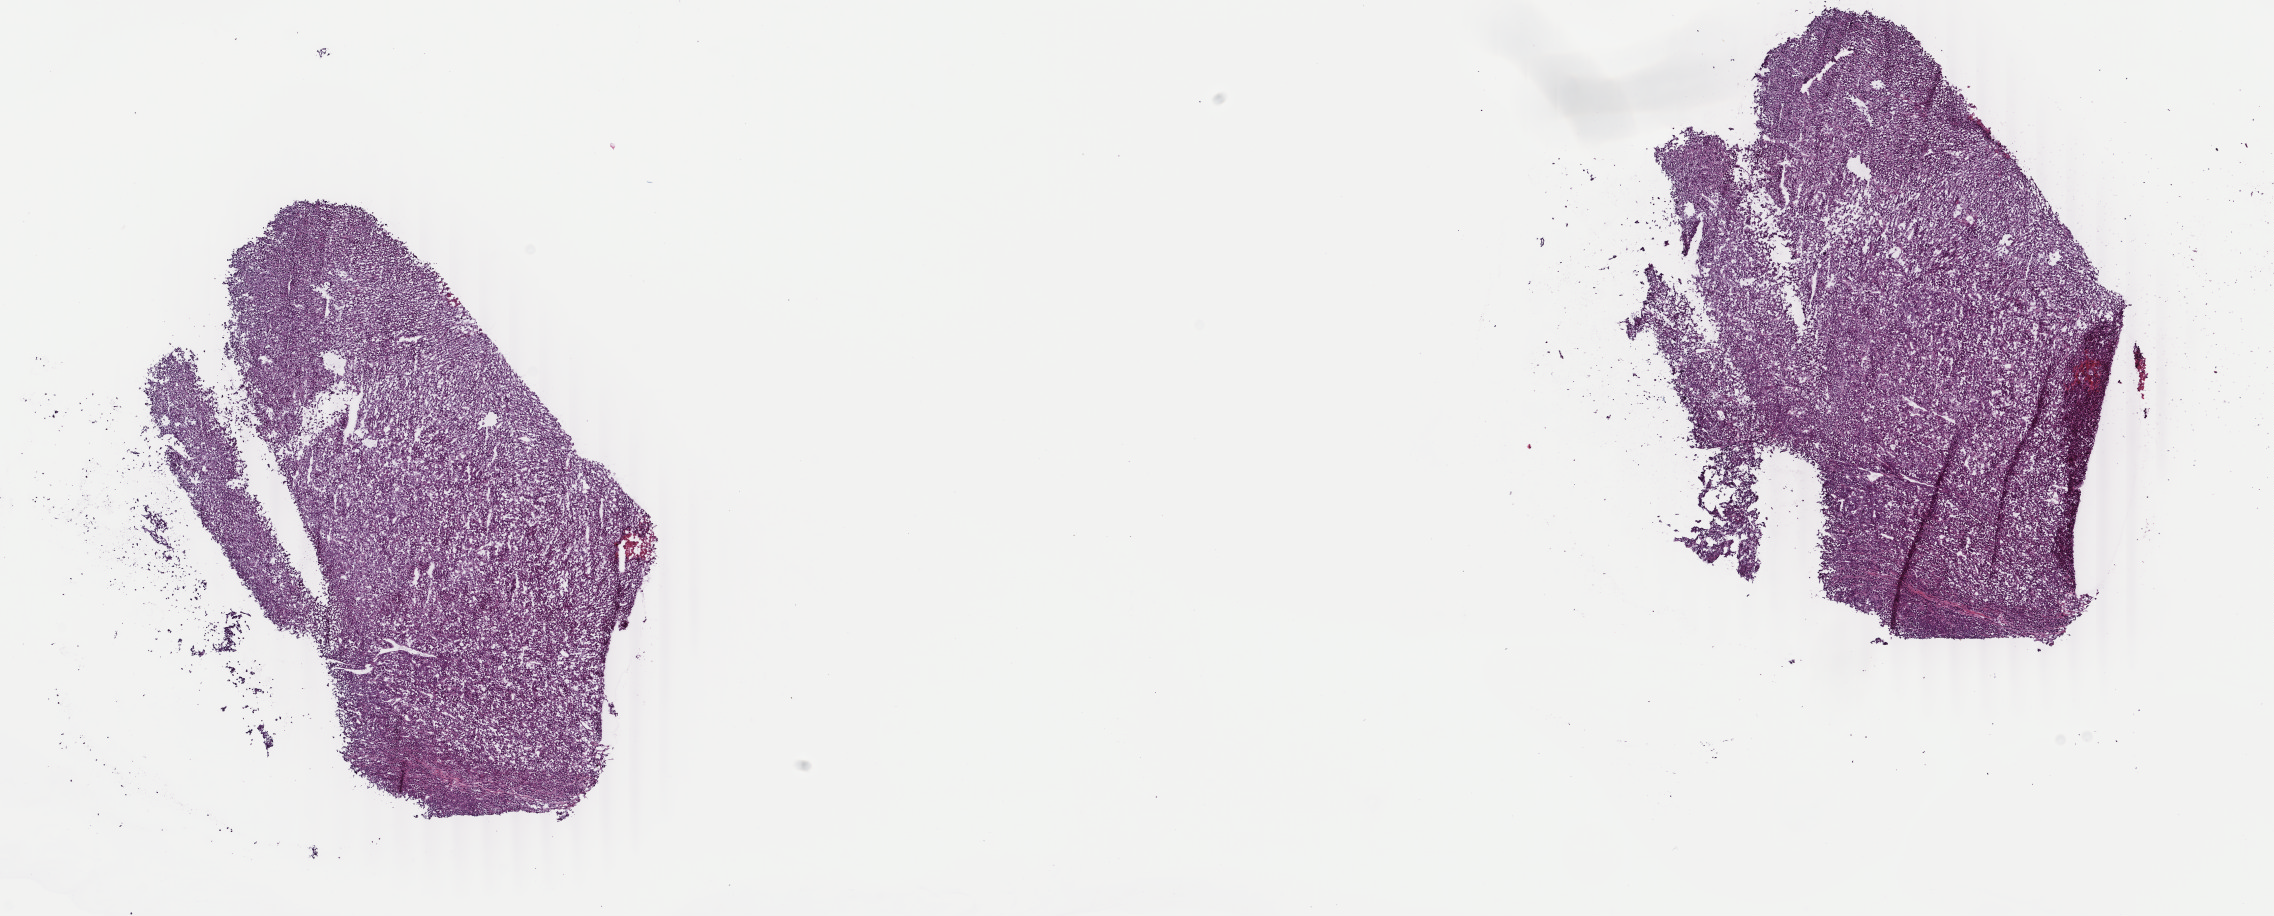
H&E-stained whole-slide image, shown as a low-resolution overview of the whole scanned area (about 18.1 x 7.3 mm, slide scanned at 40x). Frozen section from the top of the tissue portion. Sample: primary tumour, adrenal cortex. Female, age 22 years at initial diagnosis. Composition of this section per pathologist review: tumour cells 100%, tumour nuclei 80%, normal cells 0%, stromal cells 0%, necrosis 0%. Infiltration values recorded for this section: lymphocyte infiltration 2%, monocyte infiltration 0%, neutrophil infiltration 0%.
* diagnosis: Adrenal cortical carcinoma
* laterality: right